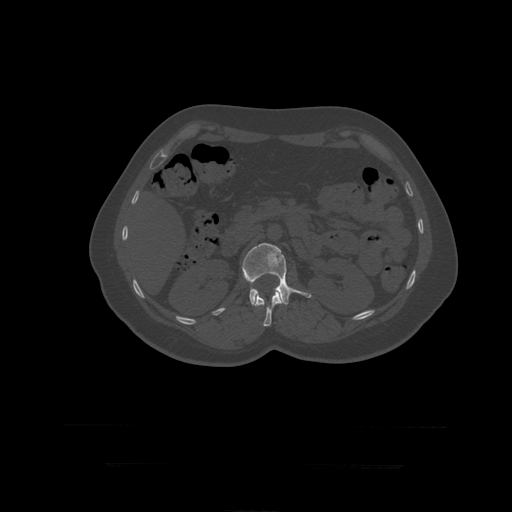
CT including the spine, one axial slice; slice 159 of 399 in the series (ordered by position); 120 kVp; bone window (W 1800 / L 400 HU); 1.25 mm slice thickness; 512 × 512 image matrix, field of view 450 × 450 mm. Patient age 41 years. From the clinical record (not read from this slice): primary cancer: breast.
Annotated regions visible in this slice (semi-automatically segmented with operator editing):
- L1 vertebra: bounding box [x1, y1, x2, y2] px = [255, 290, 284, 327]
- L2 vertebra: [242, 243, 312, 307]